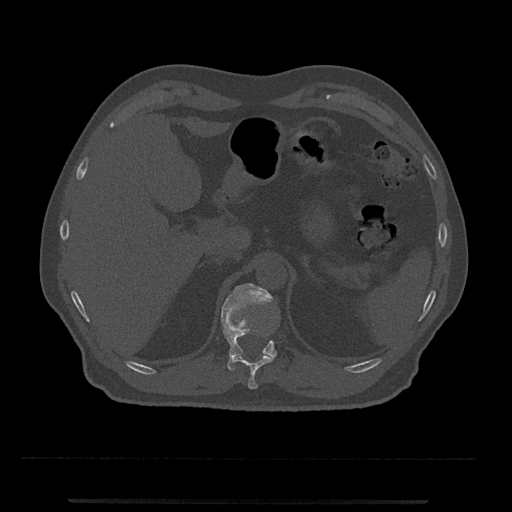
CT including the spine, one axial slice; slice 432 of 797 in the series (ordered by position); bone window (W 1800 / L 400 HU); 0.5 mm slice thickness; 512 × 512 image matrix, field of view 419 × 419 mm. Male patient, age 63 years. Case-level facts recorded for this patient, not image findings: primary cancer: prostate.
Outlined on this slice (semi-automatic segmentation, software-assisted and operator-edited):
- T11 vertebra: bounding box [x1, y1, x2, y2] px = [233, 354, 274, 389]
- T12 vertebra: [221, 283, 277, 371]